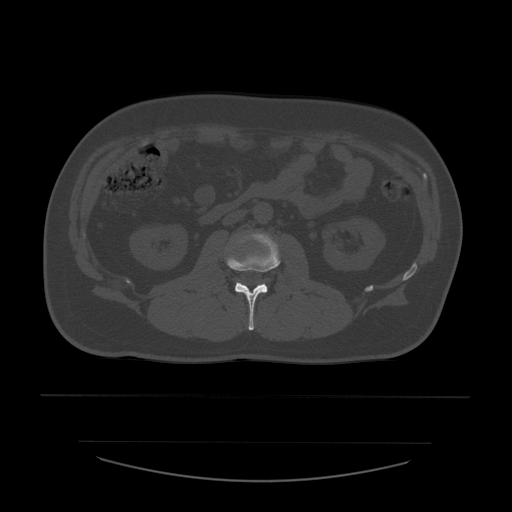
CT including the spine, one axial slice; position 193 of 532 along the scan axis; reconstruction kernel STANDARD; 120 kVp; bone window (W 1800 / L 400 HU); 512 × 512 image matrix. Patient age 44 years. Case-level facts recorded for this patient, not image findings: primary cancer: soft tissue sarcoma.
Annotated regions visible in this slice (semi-automatically segmented with operator editing):
- L2 vertebra: bounding box [x1, y1, x2, y2] px = [227, 233, 281, 331]